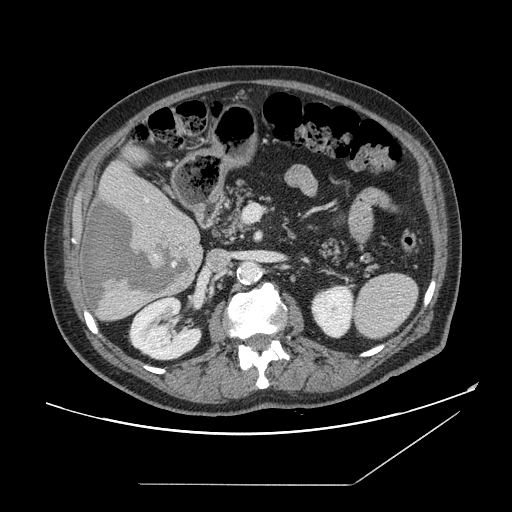
Contrast-enhanced abdominal CT, one axial slice. Position 75 of 166 along the scan axis. 120 kVp. Intravenous contrast given. Soft-tissue window (W 400 / L 40 HU). 2.5 mm slice thickness. 512 × 512 image matrix. Male patient, age 80 years. From the clinical record (not read from this slice): diagnosis: colorectal cancer liver metastases, imaged before liver resection; multiple liver metastases: no; largest metastasis: 2.2 cm; disease in both lobes: no.
Outlined on this slice (expert manual segmentation):
- hepatic veins: bounding box [x1, y1, x2, y2] px = [146, 199, 149, 202]
- liver: [80, 151, 203, 322]
- planned liver remnant (the part of the liver to remain after resection): [103, 156, 194, 227]
- liver metastasis: [84, 199, 192, 312]